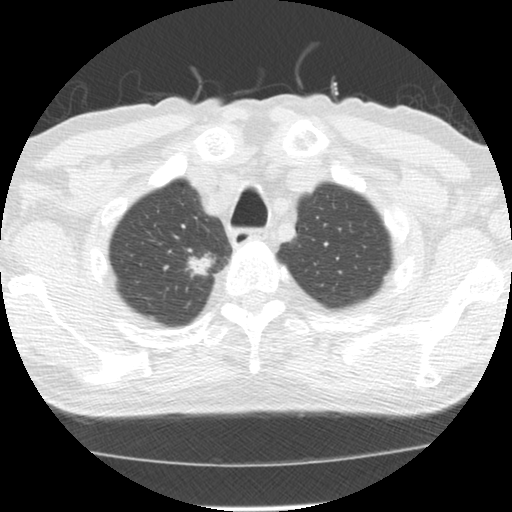
Low-dose screening chest CT, one axial slice. Slice 116 of 139 in the series (ordered by position). Reconstruction kernel STANDARD. 120 kVp. Lung window (W 1500 / L -600 HU). 2.5 mm slice thickness. 512 × 512 image matrix, field of view 310 × 310 mm.
Outlined on this slice (outlined manually by an expert reader):
- lesion 1 (tumor, upper lobe of right lung): bounding box (x1, y1, x2, y2) in pixels: (185, 252, 216, 278)